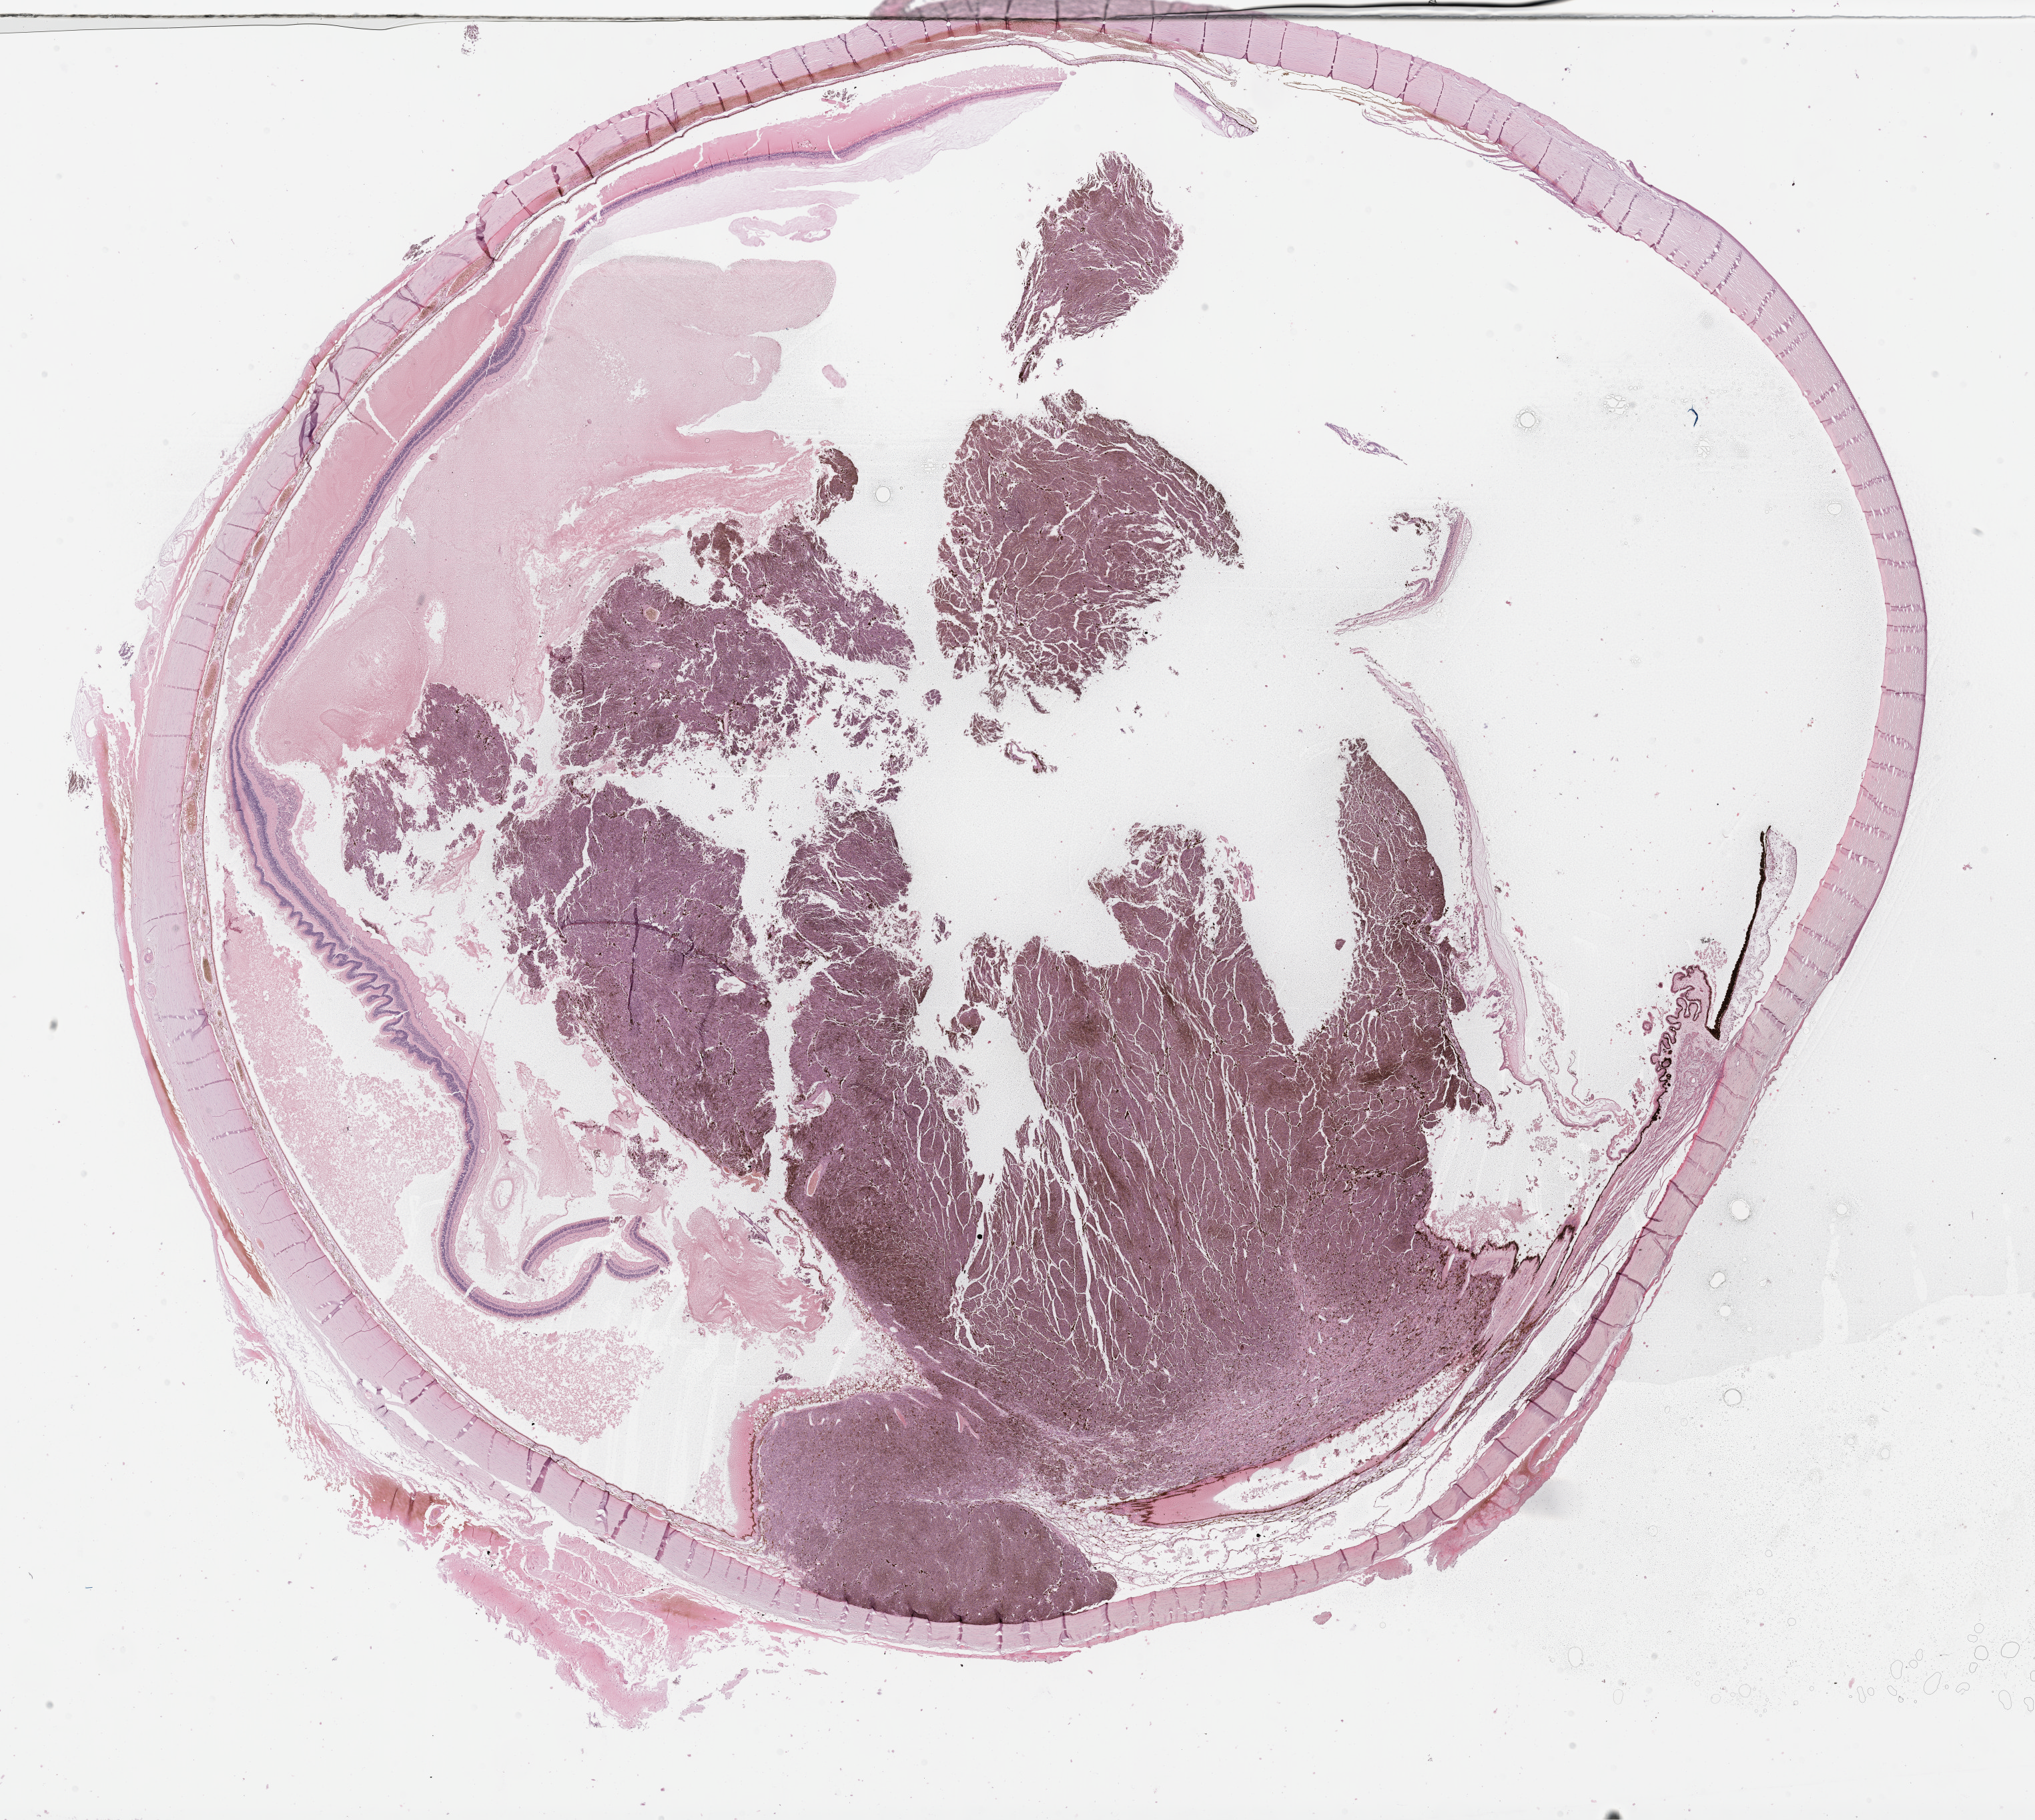
Digitized Hematoxylin and eosin (H&E) stained tissue section (whole slide) — low-resolution overview of the scanned area, about 24.7 x 22.1 mm. Formalin-fixed paraffin-embedded (FFPE) diagnostic section. Uvea, primary tumour sample. Male patient; age at initial diagnosis 64 years.
Histologic diagnosis: Mixed epithelioid and spindle cell melanoma (choroid).